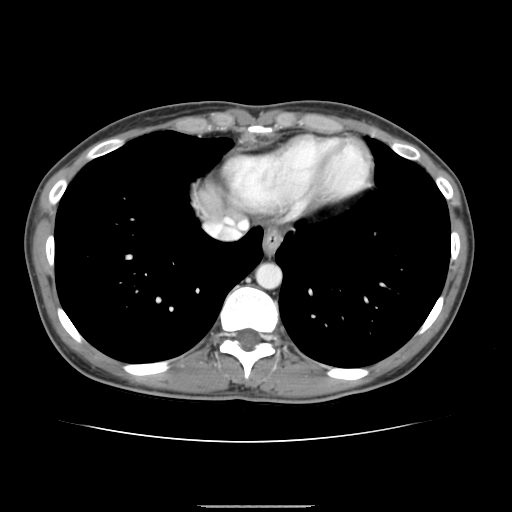
Contrast-enhanced abdominal CT, one axial slice. Position 138 of 150 along the scan axis. 120 kVp. Intravenous contrast given. Soft-tissue window (W 400 / L 40 HU). 2.5 mm slice thickness. 512 × 512 image matrix, field of view 324 × 324 mm. Female patient, age 32 years. From the clinical record (not read from this slice): diagnosis: colorectal cancer liver metastases, imaged before liver resection; multiple liver metastases: yes; largest metastasis: 0.7 cm; chemotherapy before resection: yes.
Annotated regions visible in this slice (outlined manually by an expert reader):
- liver: bounding box (x1, y1, x2, y2) in pixels: (201, 189, 231, 219)
- planned liver remnant (the part of the liver to remain after resection): (201, 189, 230, 219)